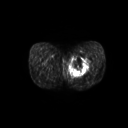
FDG PET of an extremity soft-tissue mass (from a PET/CT study), one axial slice; slice 28 of 267 in the series (ordered by position); 3.27 mm slice thickness; 128 × 128 image matrix, field of view 600 × 600 mm. Male patient, age 59 years. From the clinical record (not read from this slice): histological type: pleiomorphic liposarcoma; grade: high; site of the primary tumour: left thigh.
Structures marked on this image (expert contour drawn on MRI and transferred to this co-registered scan by the dataset authors):
- gross tumour volume including surrounding oedema: box from (x=69, y=56) to (x=91, y=77) px
- gross tumour volume (mass): (x=70, y=57)–(x=90, y=76)